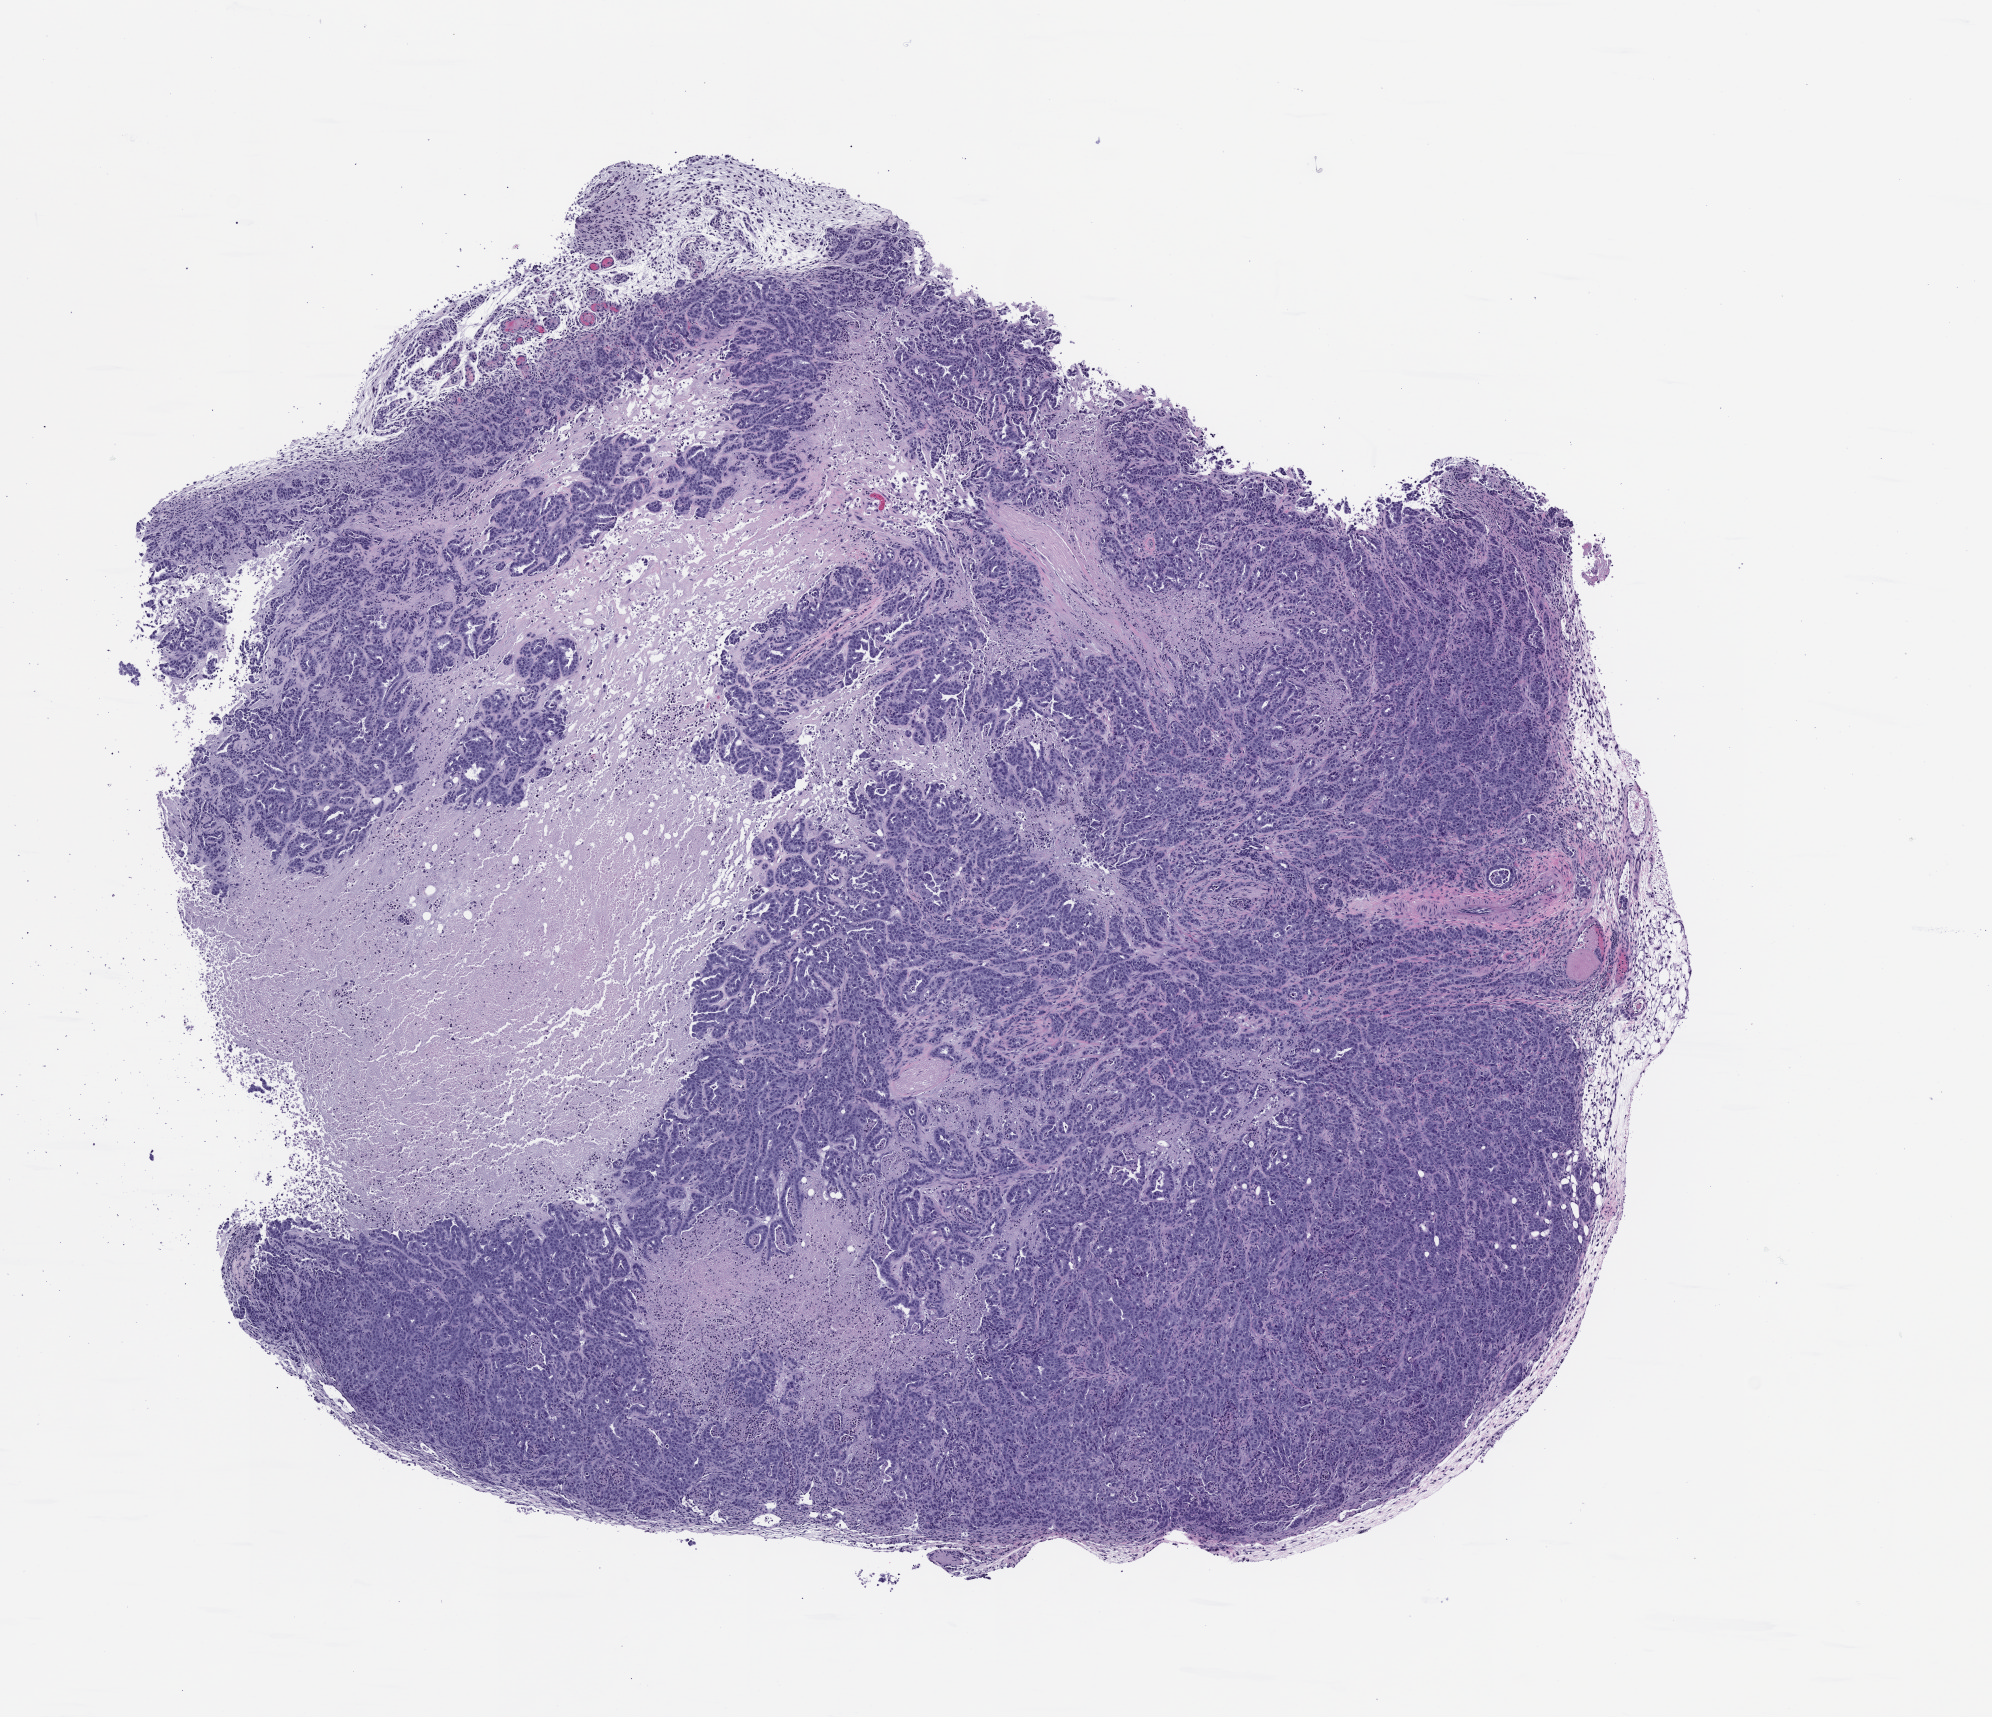
Whole-slide image, haematoxylin and eosin: patient-derived xenograft (human tumor grown in a mouse) — whole scanned area (about 8.0 x 6.9 mm) shown as a low-resolution overview, formalin-fixed paraffin-embedded section, tumor site category: lung.
Originating patient diagnosis: Lung Adenocarcinoma.